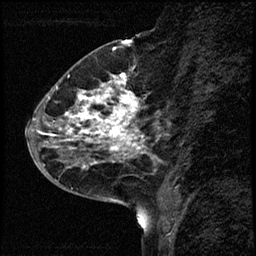
Breast MRI (dynamic contrast-enhanced), one sagittal slice; position 23 of 68 along the scan axis; dynamic contrast-enhanced study with each time point stored as its own series, time point 2 of 3 at this slice position (early post-contrast, ordered by acquisition time); 1.5 T; TE 4.2 ms, TR 17.6 ms; 2 mm slice thickness; 256 × 256 image matrix, field of view 200 × 200 mm. Female patient, age 52 years. Case-level facts recorded for this patient, not image findings: setting: breast cancer imaged before/during neoadjuvant chemotherapy; receptor status: HER2-positive.
Annotated regions visible in this slice (semi-automatic segmentation, software-assisted and operator-edited):
- analysis volume of interest (the breast-tissue region the enhancement analysis was run in; not a lesion): bounding box (x1, y1, x2, y2) in pixels: (50, 61, 162, 184)
- tumour enhancement mask (voxels above the 100 % enhancement threshold inside the analysis volume of interest): (53, 73, 143, 157)